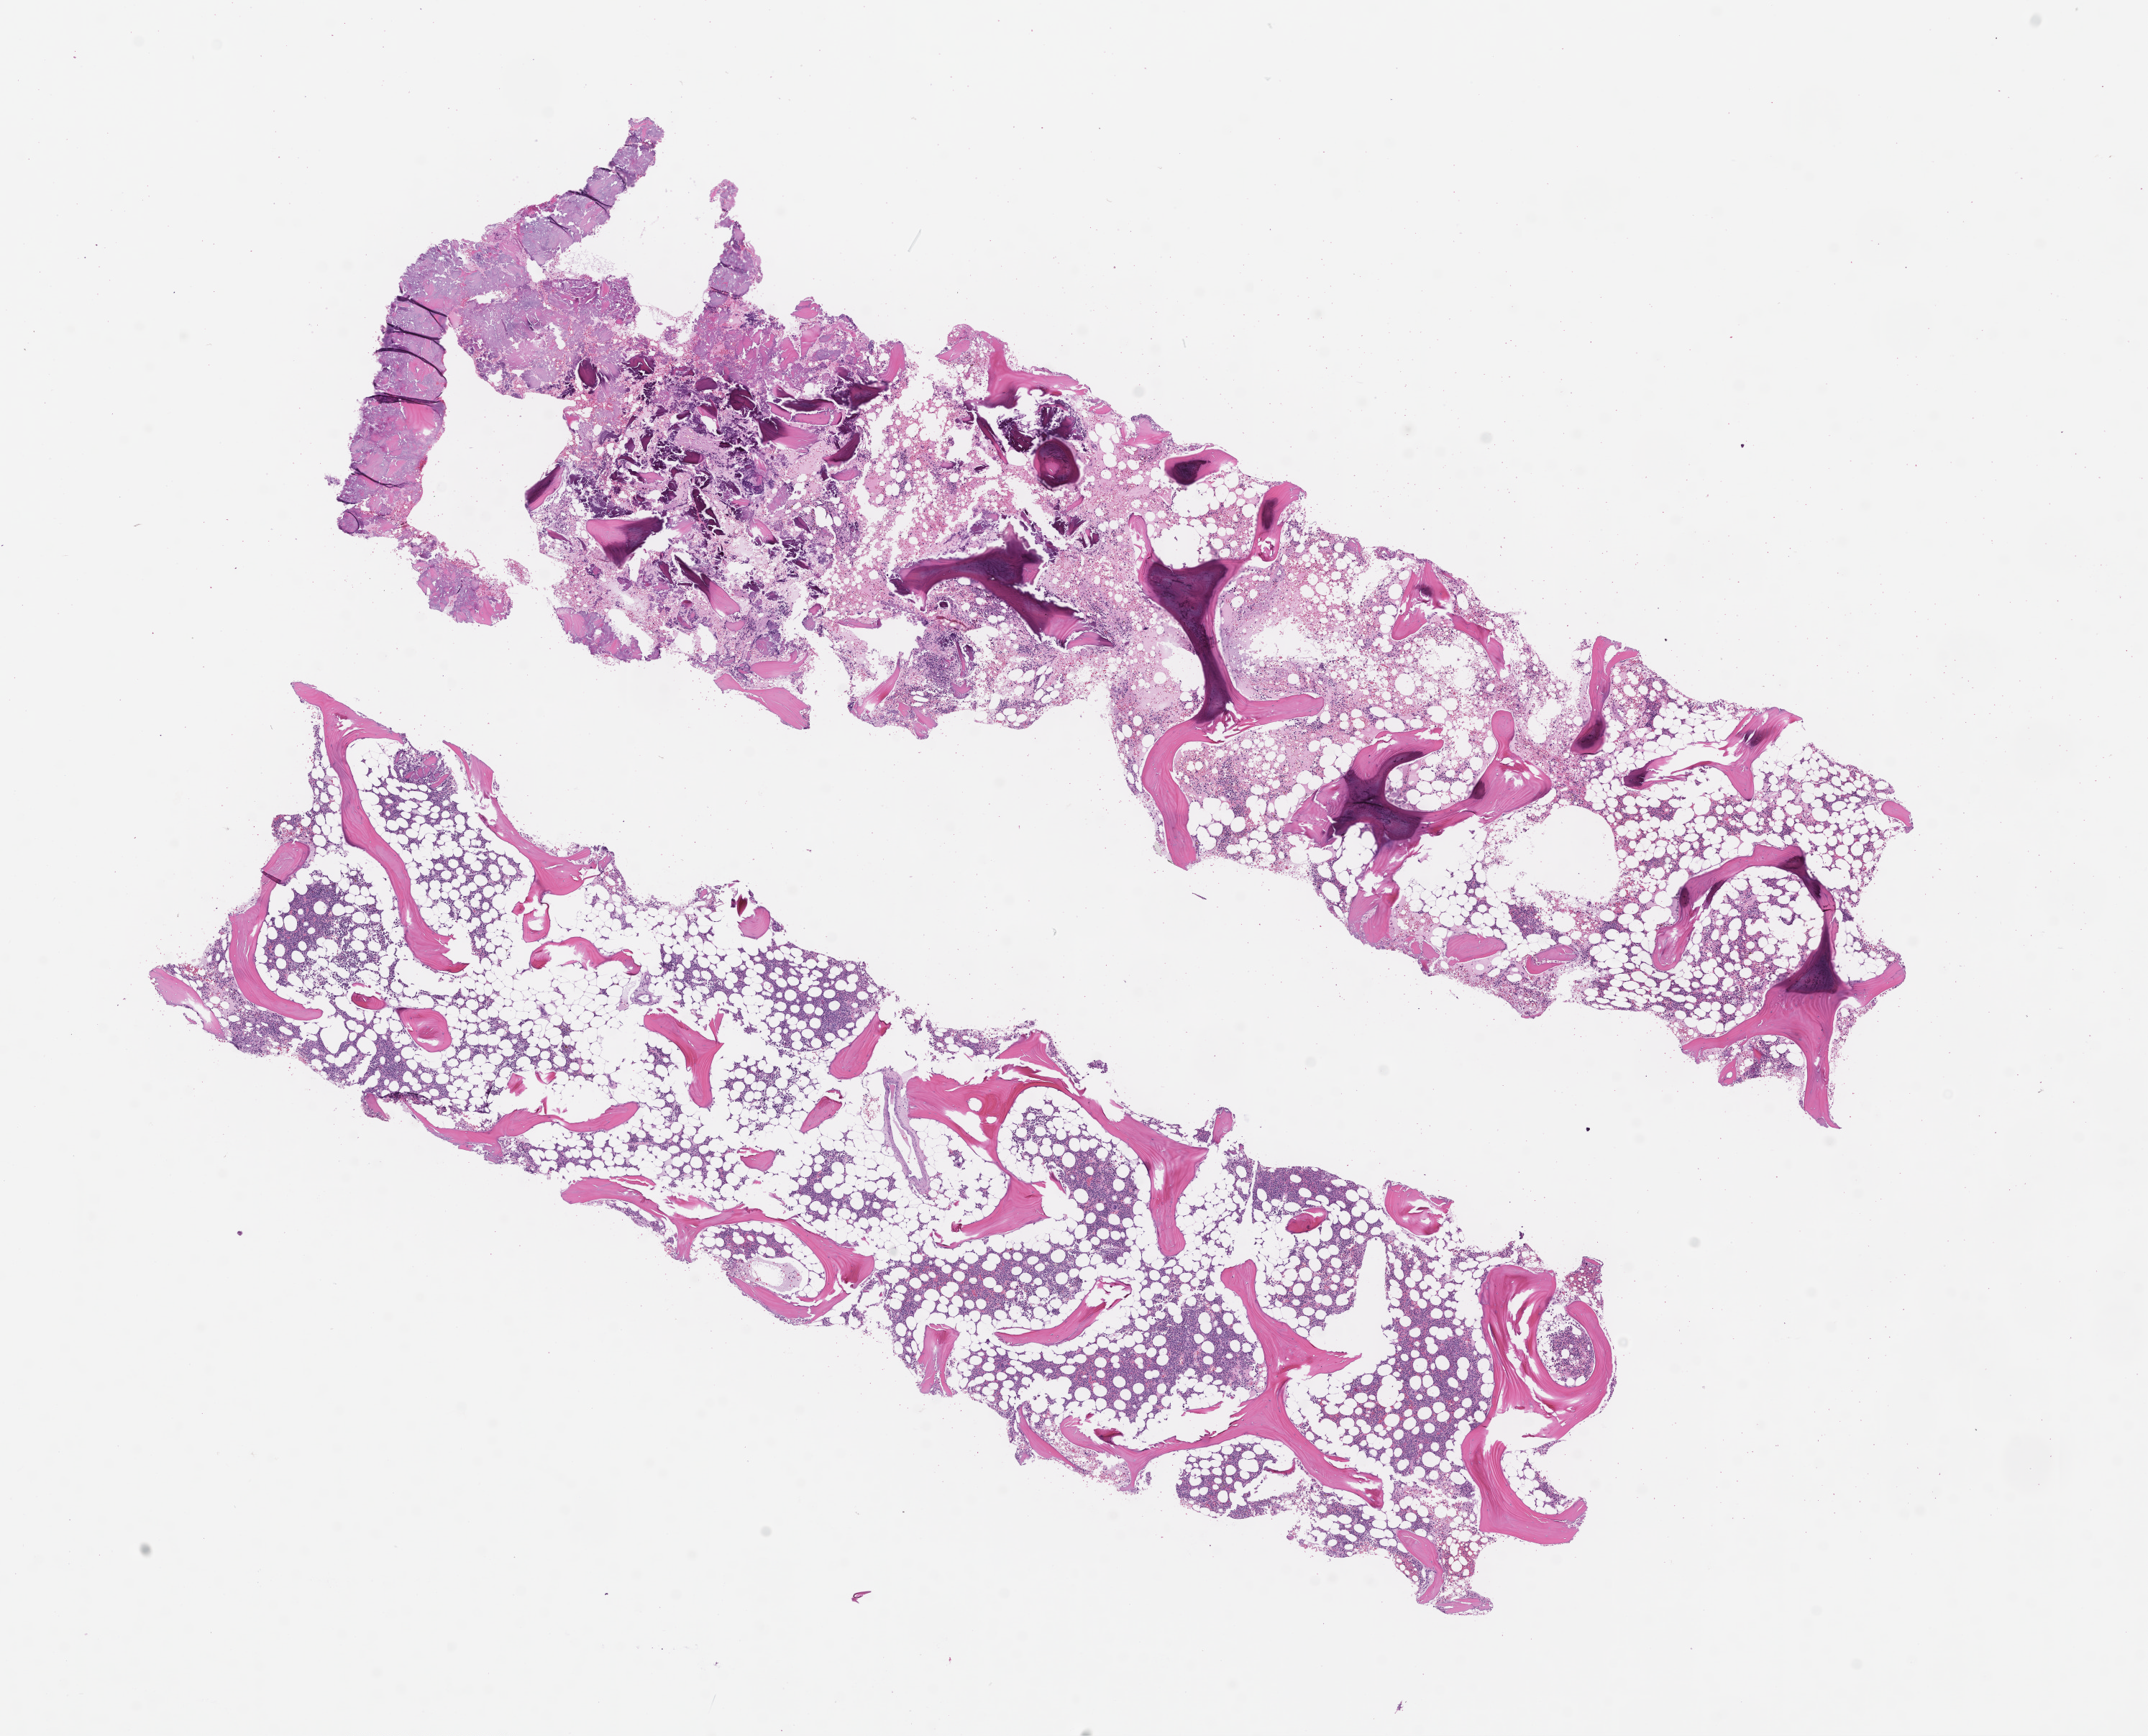
Digitized haematoxylin and eosin-stained section, low-resolution overview of the scanned area, about 12.1 x 9.7 mm. FFPE section. Site: bone marrow. Archival tissue. Patient sex: female.
This section: primary tumor. Diagnosis: Plasma Cell Myeloma.